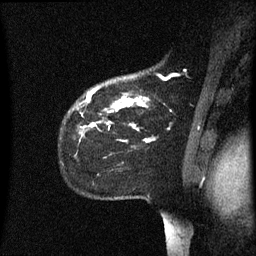
Breast MRI (dynamic contrast-enhanced), one sagittal slice. Position 47 of 60 along the scan axis. Dynamic contrast-enhanced series, image 2 of 3 at this slice position (ordered by acquisition). 1.5 T. TE 4.2 ms, TR 8.4 ms. 2.2 mm slice thickness. 256 × 256 image matrix, field of view 200 × 200 mm. Patient: female, 35 years. From the clinical record (not read from this slice): setting: breast cancer imaged before/during neoadjuvant chemotherapy; receptor status: HER2-positive.
Structures marked on this image (semi-automatically segmented with operator editing):
- analysis volume of interest (the breast-tissue region the enhancement analysis was run in; not a lesion): bounding box [x1, y1, x2, y2] px = [69, 78, 151, 159]
- tumour enhancement mask (voxels above the 70 % enhancement threshold inside the analysis volume of interest): [88, 96, 150, 143]